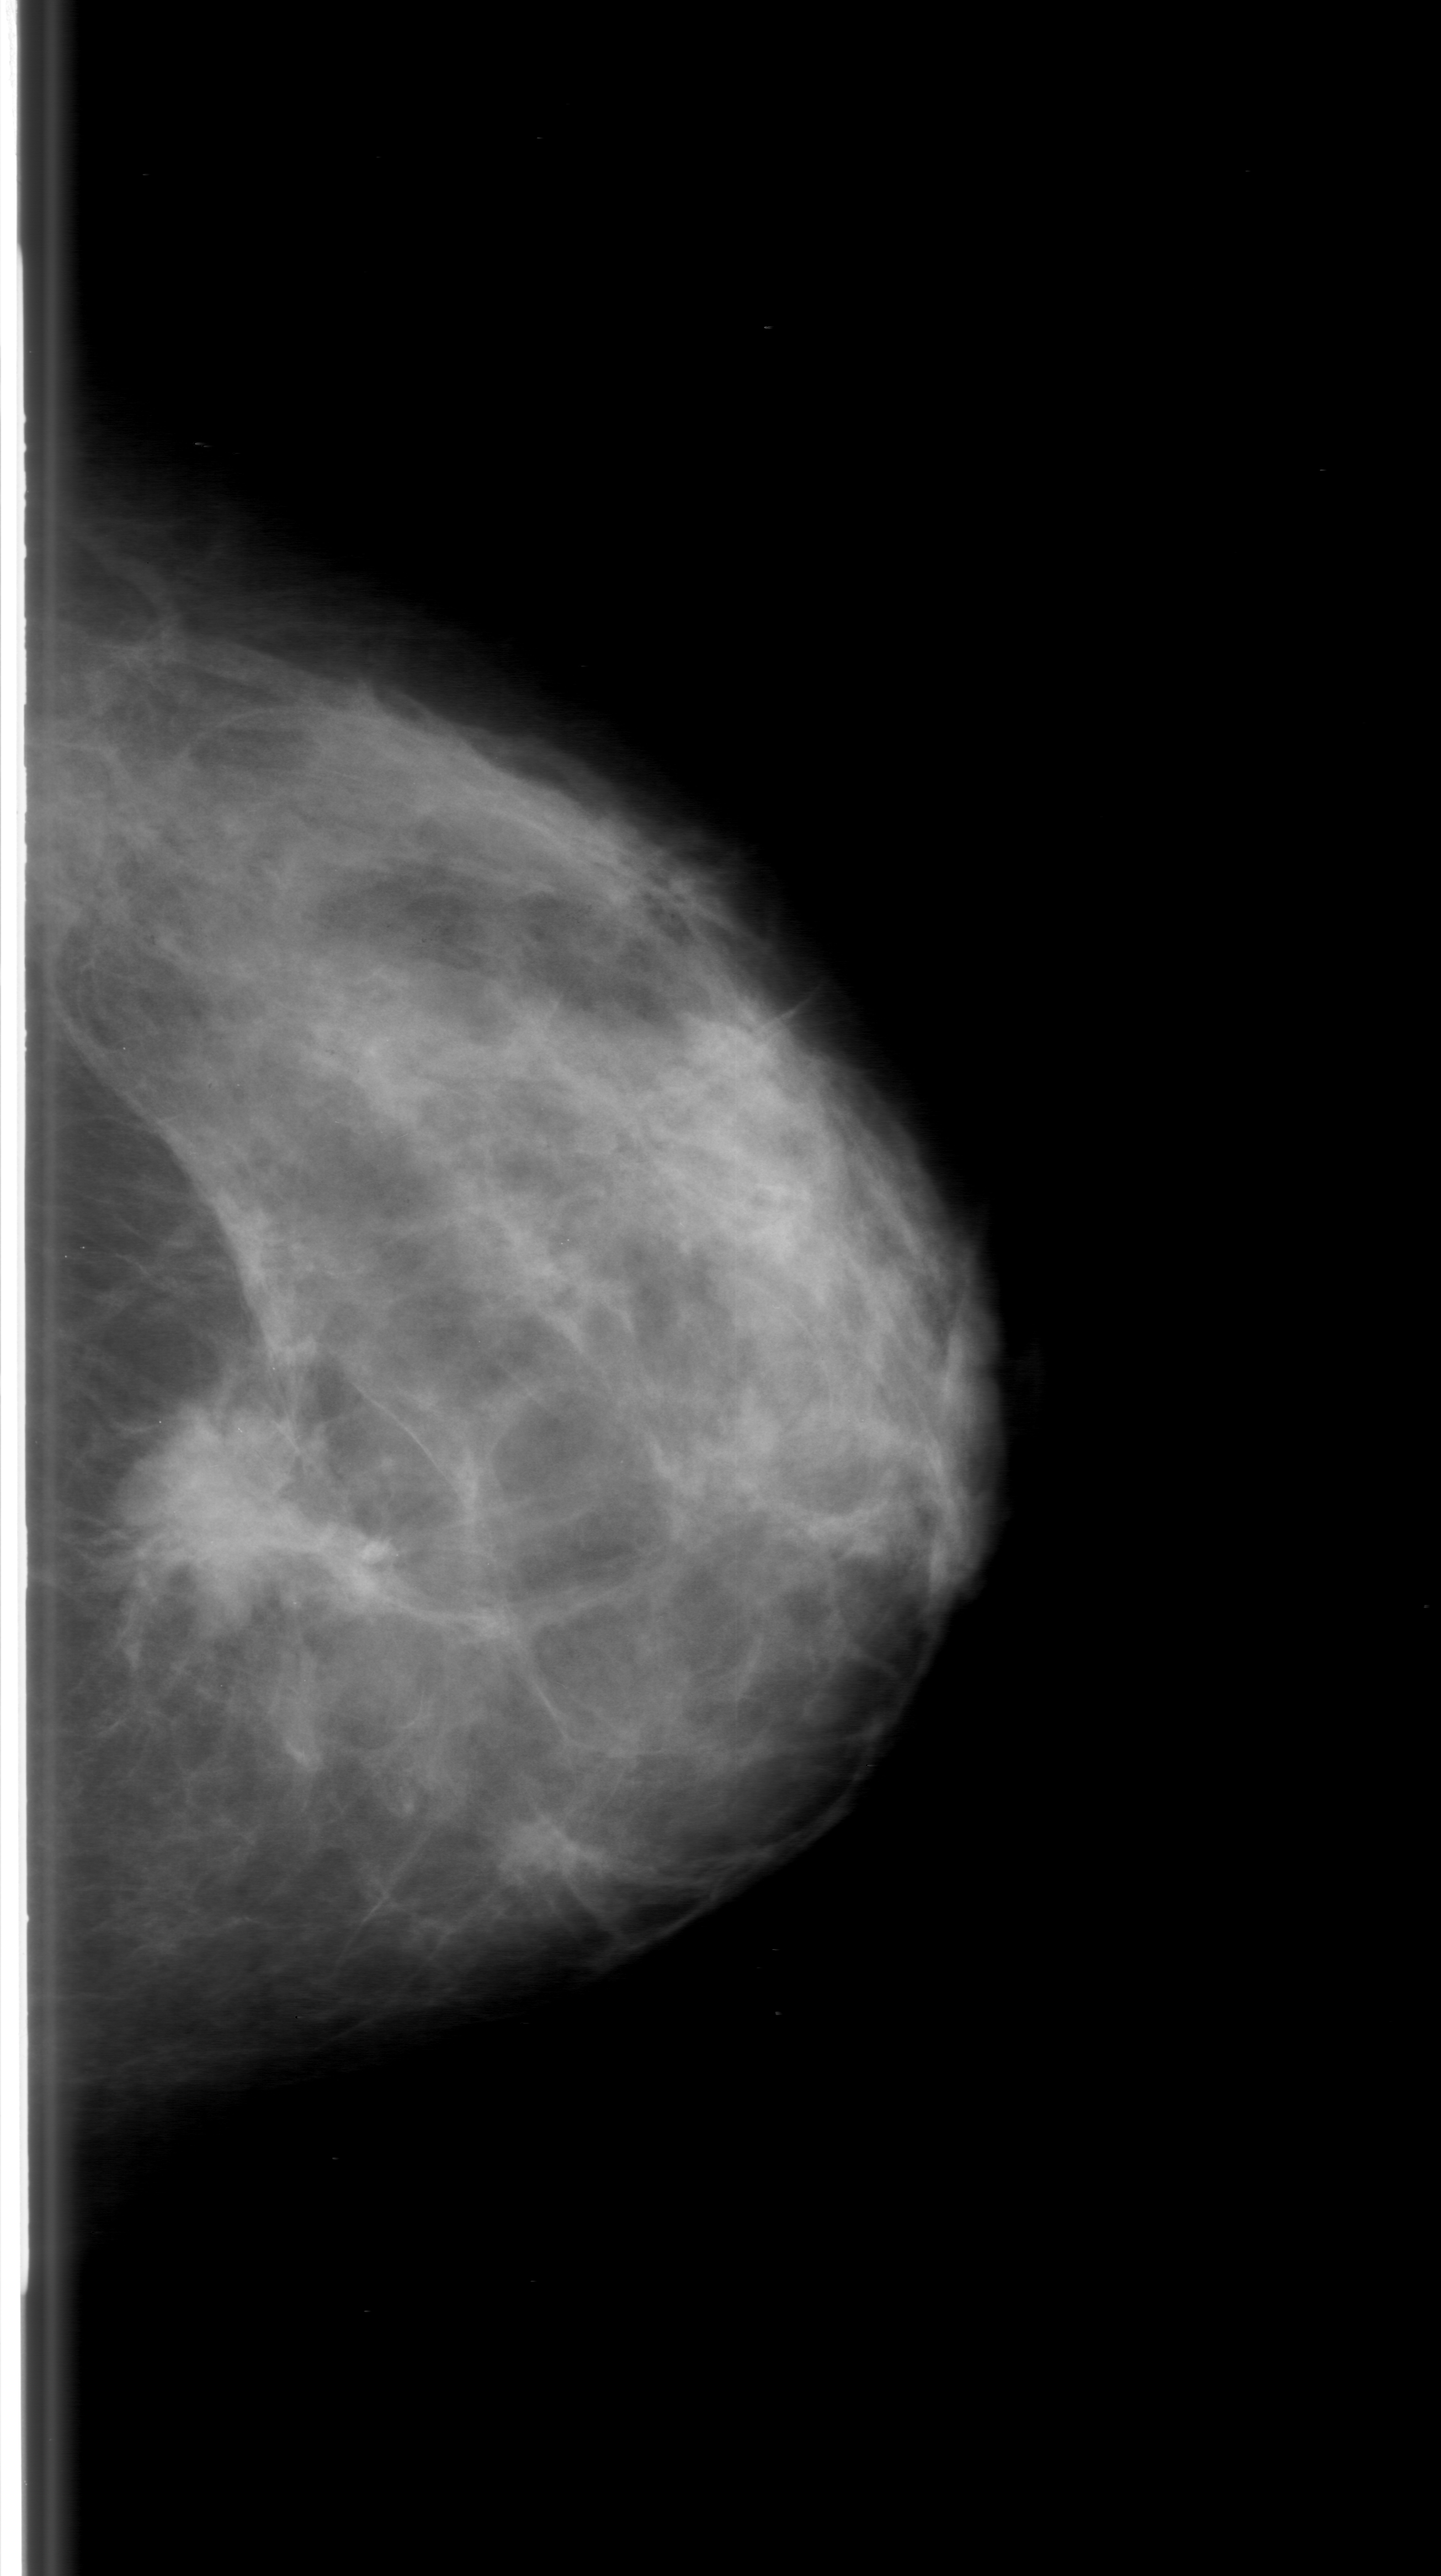
Mammogram (digitized film); left breast; craniocaudal (CC) view; 1441 × 2576 image matrix.
Expert-marked regions of interest on this image (one box per marked abnormality):
- mass, shape irregular, margins spiculated; BI-RADS assessment category 5; subtlety rating 4 on a 1 (subtle) to 5 (obvious) scale; pathology (as recorded): malignant: box from (x=145, y=1429) to (x=394, y=1631) px